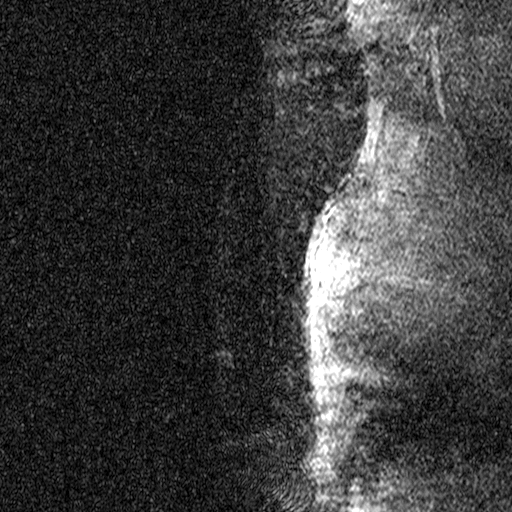
Breast MRI (dynamic contrast-enhanced), one sagittal slice; slice 41 of 44 in the series (ordered by position); dynamic contrast-enhanced study with each time point stored as its own series, time point 2 of 3 at this slice position (early post-contrast, ordered by acquisition time); 1.5 T; TE 4.5 ms, TR 11 ms; 3 mm slice thickness; 512 × 512 image matrix, field of view 200 × 200 mm. Female patient, age 44 years. From the clinical record (not read from this slice): setting: breast cancer imaged before/during neoadjuvant chemotherapy; receptor status: HR-positive, HER2-negative.
Structures marked on this image (semi-automatic segmentation, software-assisted and operator-edited):
- analysis volume of interest (the breast-tissue region the enhancement analysis was run in; not a lesion): bounding box (x1, y1, x2, y2) in pixels: (218, 118, 341, 291)
- tumour enhancement mask (voxels above the 90 % enhancement threshold inside the analysis volume of interest): (316, 217, 325, 283)